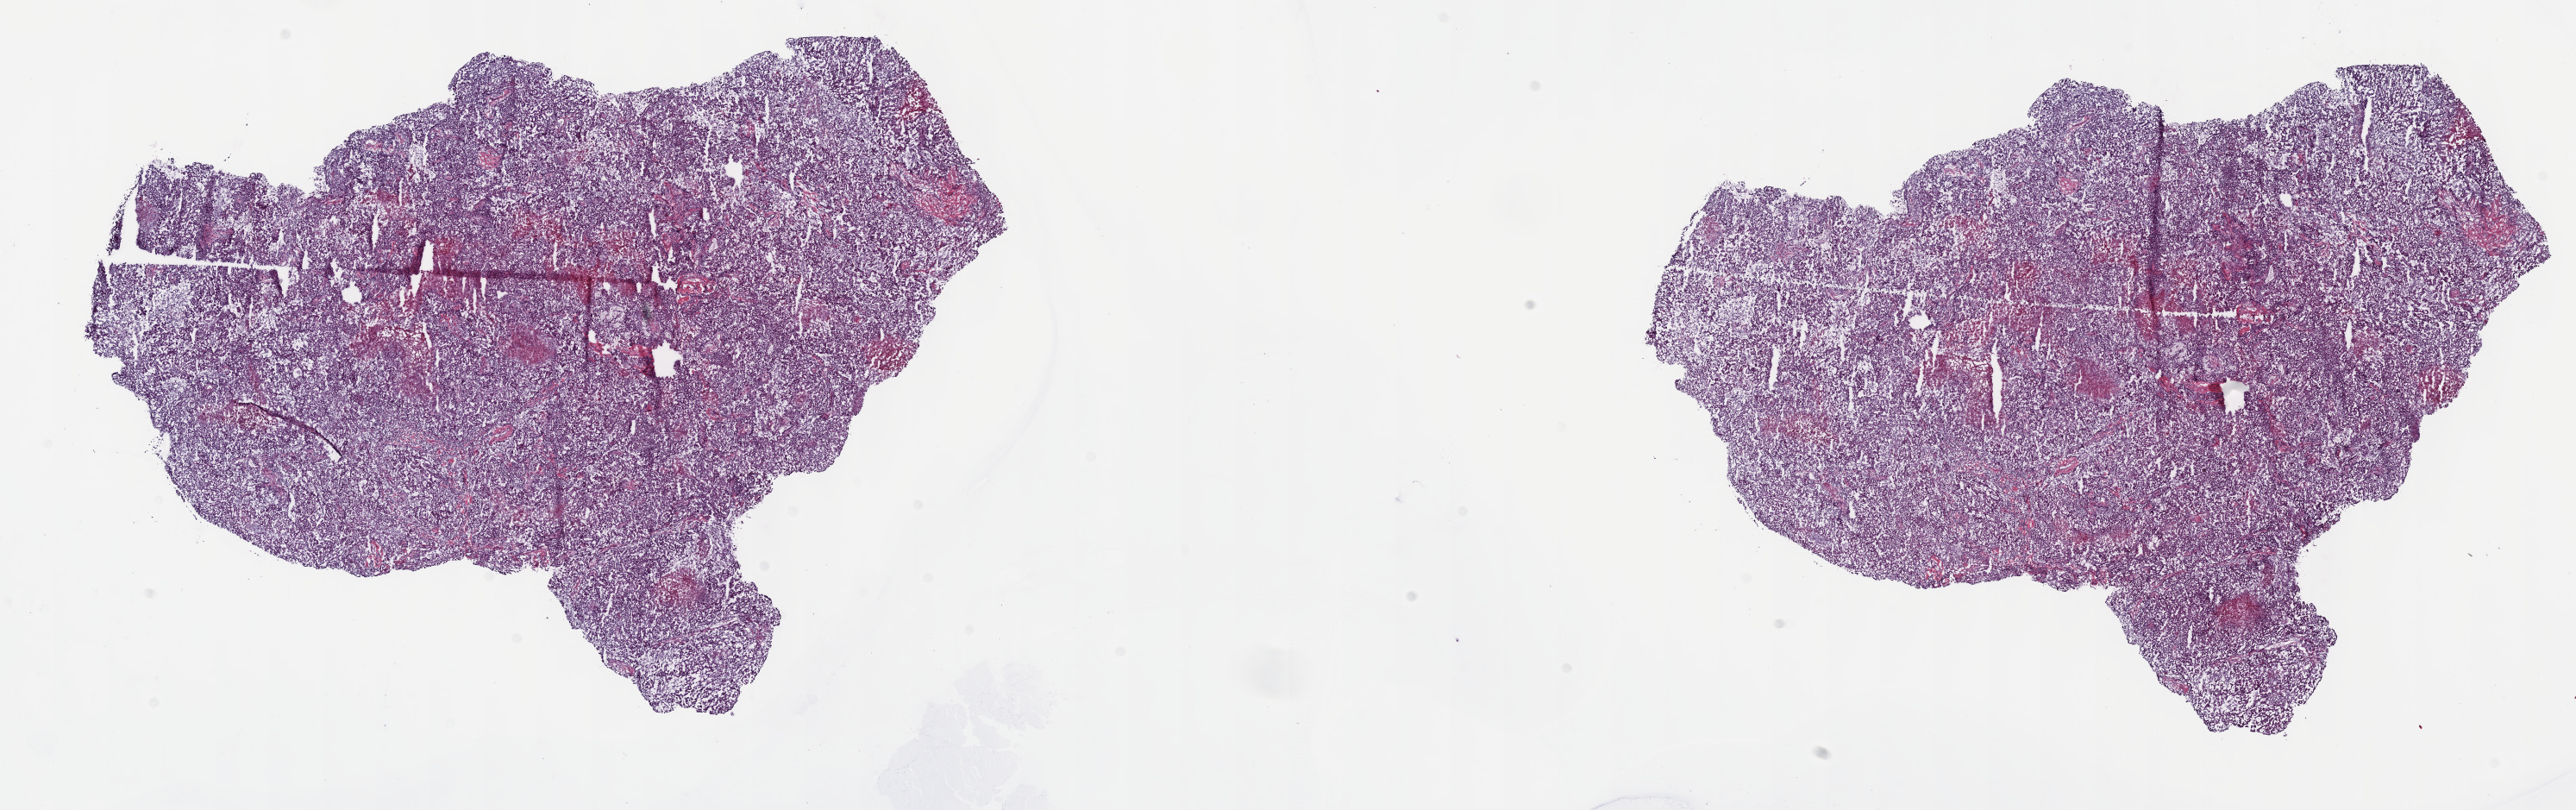
Hematoxylin and eosin (H&E) stained whole-slide image — a low-resolution overview of the entire scanned area, about 24.2 x 7.6 mm (from a 40x scan), frozen section from the top of the tissue portion, sample: primary tumour, mesothelium. Male patient; age at initial diagnosis 36 years. Pathologist review of this section (percent, as recorded): tumour cells 90%, tumour nuclei 90%, normal cells 0%, stromal cells 10%, necrosis 0%. Inflammatory infiltration, as recorded: lymphocyte infiltration 60%, monocyte infiltration 10%, neutrophil infiltration 10%.
Laterality: right. TNM: T4 N2 M1. AJCC pathologic stage: IV (7th edition). Pathologic diagnosis: Epithelioid mesothelioma, malignant (pleura, NOS).